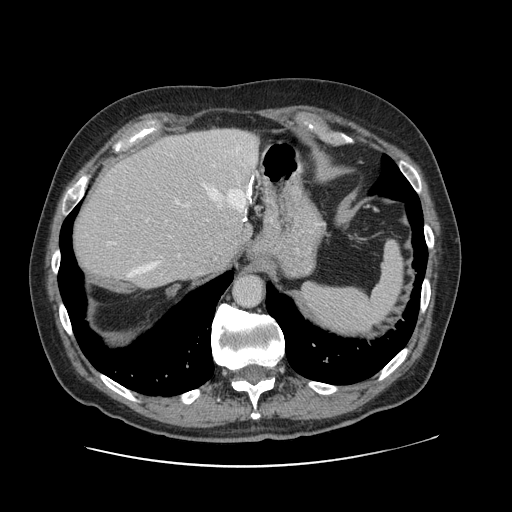
Contrast-enhanced abdominal CT, one axial slice. 120 kVp. Intravenous contrast given. Soft-tissue window (W 400 / L 40 HU). 2.5 mm slice thickness. 512 × 512 image matrix. Male patient, age 71 years. From the clinical record (not read from this slice): diagnosis: colorectal cancer liver metastases, imaged before liver resection; multiple liver metastases: no; largest metastasis: 3.3 cm; chemotherapy before resection: no.
Outlined on this slice (outlined manually by an expert reader):
- hepatic veins: bounding box <128,177,254,277> (left, top, right, bottom; pixels)
- liver: <73,130,258,288>
- planned liver remnant (the part of the liver to remain after resection): <73,155,240,289>
- portal vein (with intrahepatic branches): <109,242,116,244>